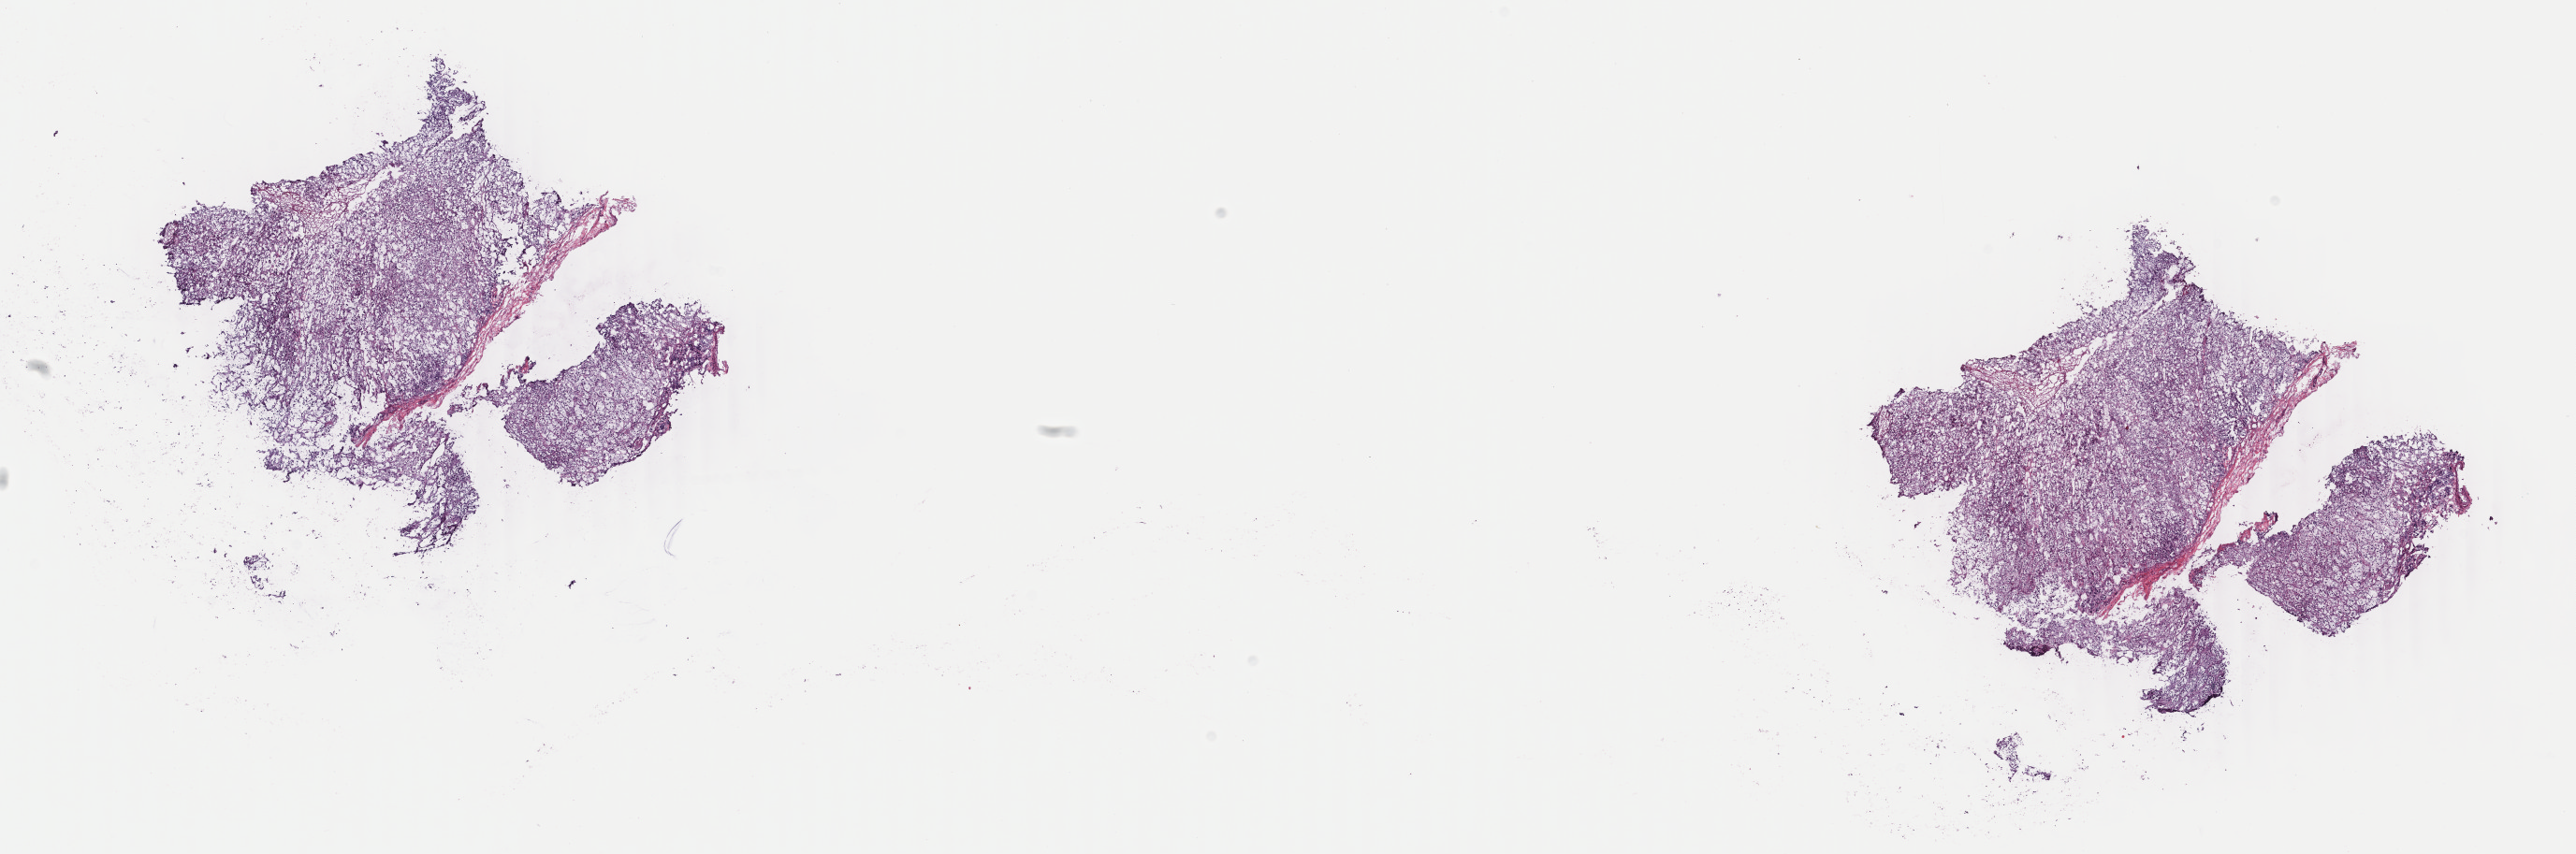
H&E whole-slide image, low-resolution overview of the scanned area, about 21.9 x 7.3 mm (from a 40x scan). Frozen section from the top of the tissue portion. Primary tumour sample from the adrenal gland. Patient: female, age at initial diagnosis 64 years. Slide review estimates, as recorded: tumour cells 95%, tumour nuclei 80%, normal cells 5%, stromal cells 0%, necrosis 0%. Infiltration values recorded for this section: lymphocyte infiltration 1%, monocyte infiltration 0%, neutrophil infiltration 0%.
Laterality: left. Pathologic diagnosis: Pheochromocytoma, malignant.